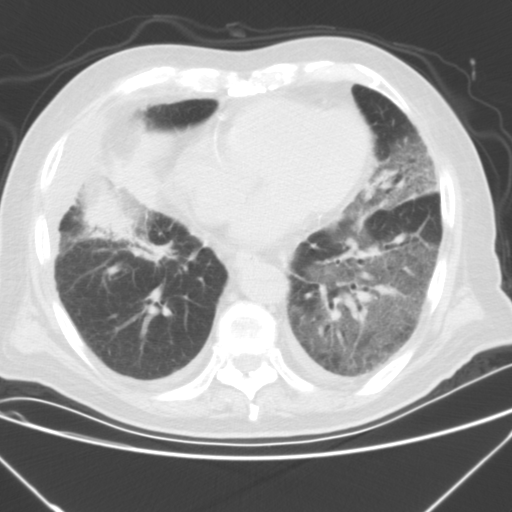
Chest CT, one axial slice; slice 10 of 43 in the series (ordered by position); 120 kVp; lung window (W 1500 / L -600 HU); 512 × 512 image matrix. Patient: male, 85 years. Case-level facts recorded for this patient, not image findings: clinical TNM (as recorded): T4 N3 M2.
Annotated regions visible in this slice (bounding box drawn by a radiologist):
- lung tumour (recorded histology: squamous cell carcinoma): box from (x=109, y=132) to (x=177, y=213) px